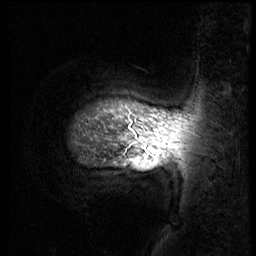
Breast MRI (dynamic contrast-enhanced), one sagittal slice. Slice 49 of 56 in the series (ordered by position). 3 images stored at this slice position (order not interpretable as contrast timing). 1.5 T. TE 4.2 ms, TR 8.9 ms. 3 mm slice thickness. 256 × 256 image matrix, field of view 220 × 220 mm. Female patient, age 57 years. From the clinical record (not read from this slice): setting: breast cancer imaged before/during neoadjuvant chemotherapy; receptor status: HER2-positive.
Structures marked on this image (semi-automatically segmented with operator editing):
- analysis volume of interest (the breast-tissue region the enhancement analysis was run in; not a lesion): box from (x=69, y=70) to (x=228, y=156) px
- tumour enhancement mask (voxels above the 140 % enhancement threshold inside the analysis volume of interest): (x=149, y=151)–(x=151, y=153)